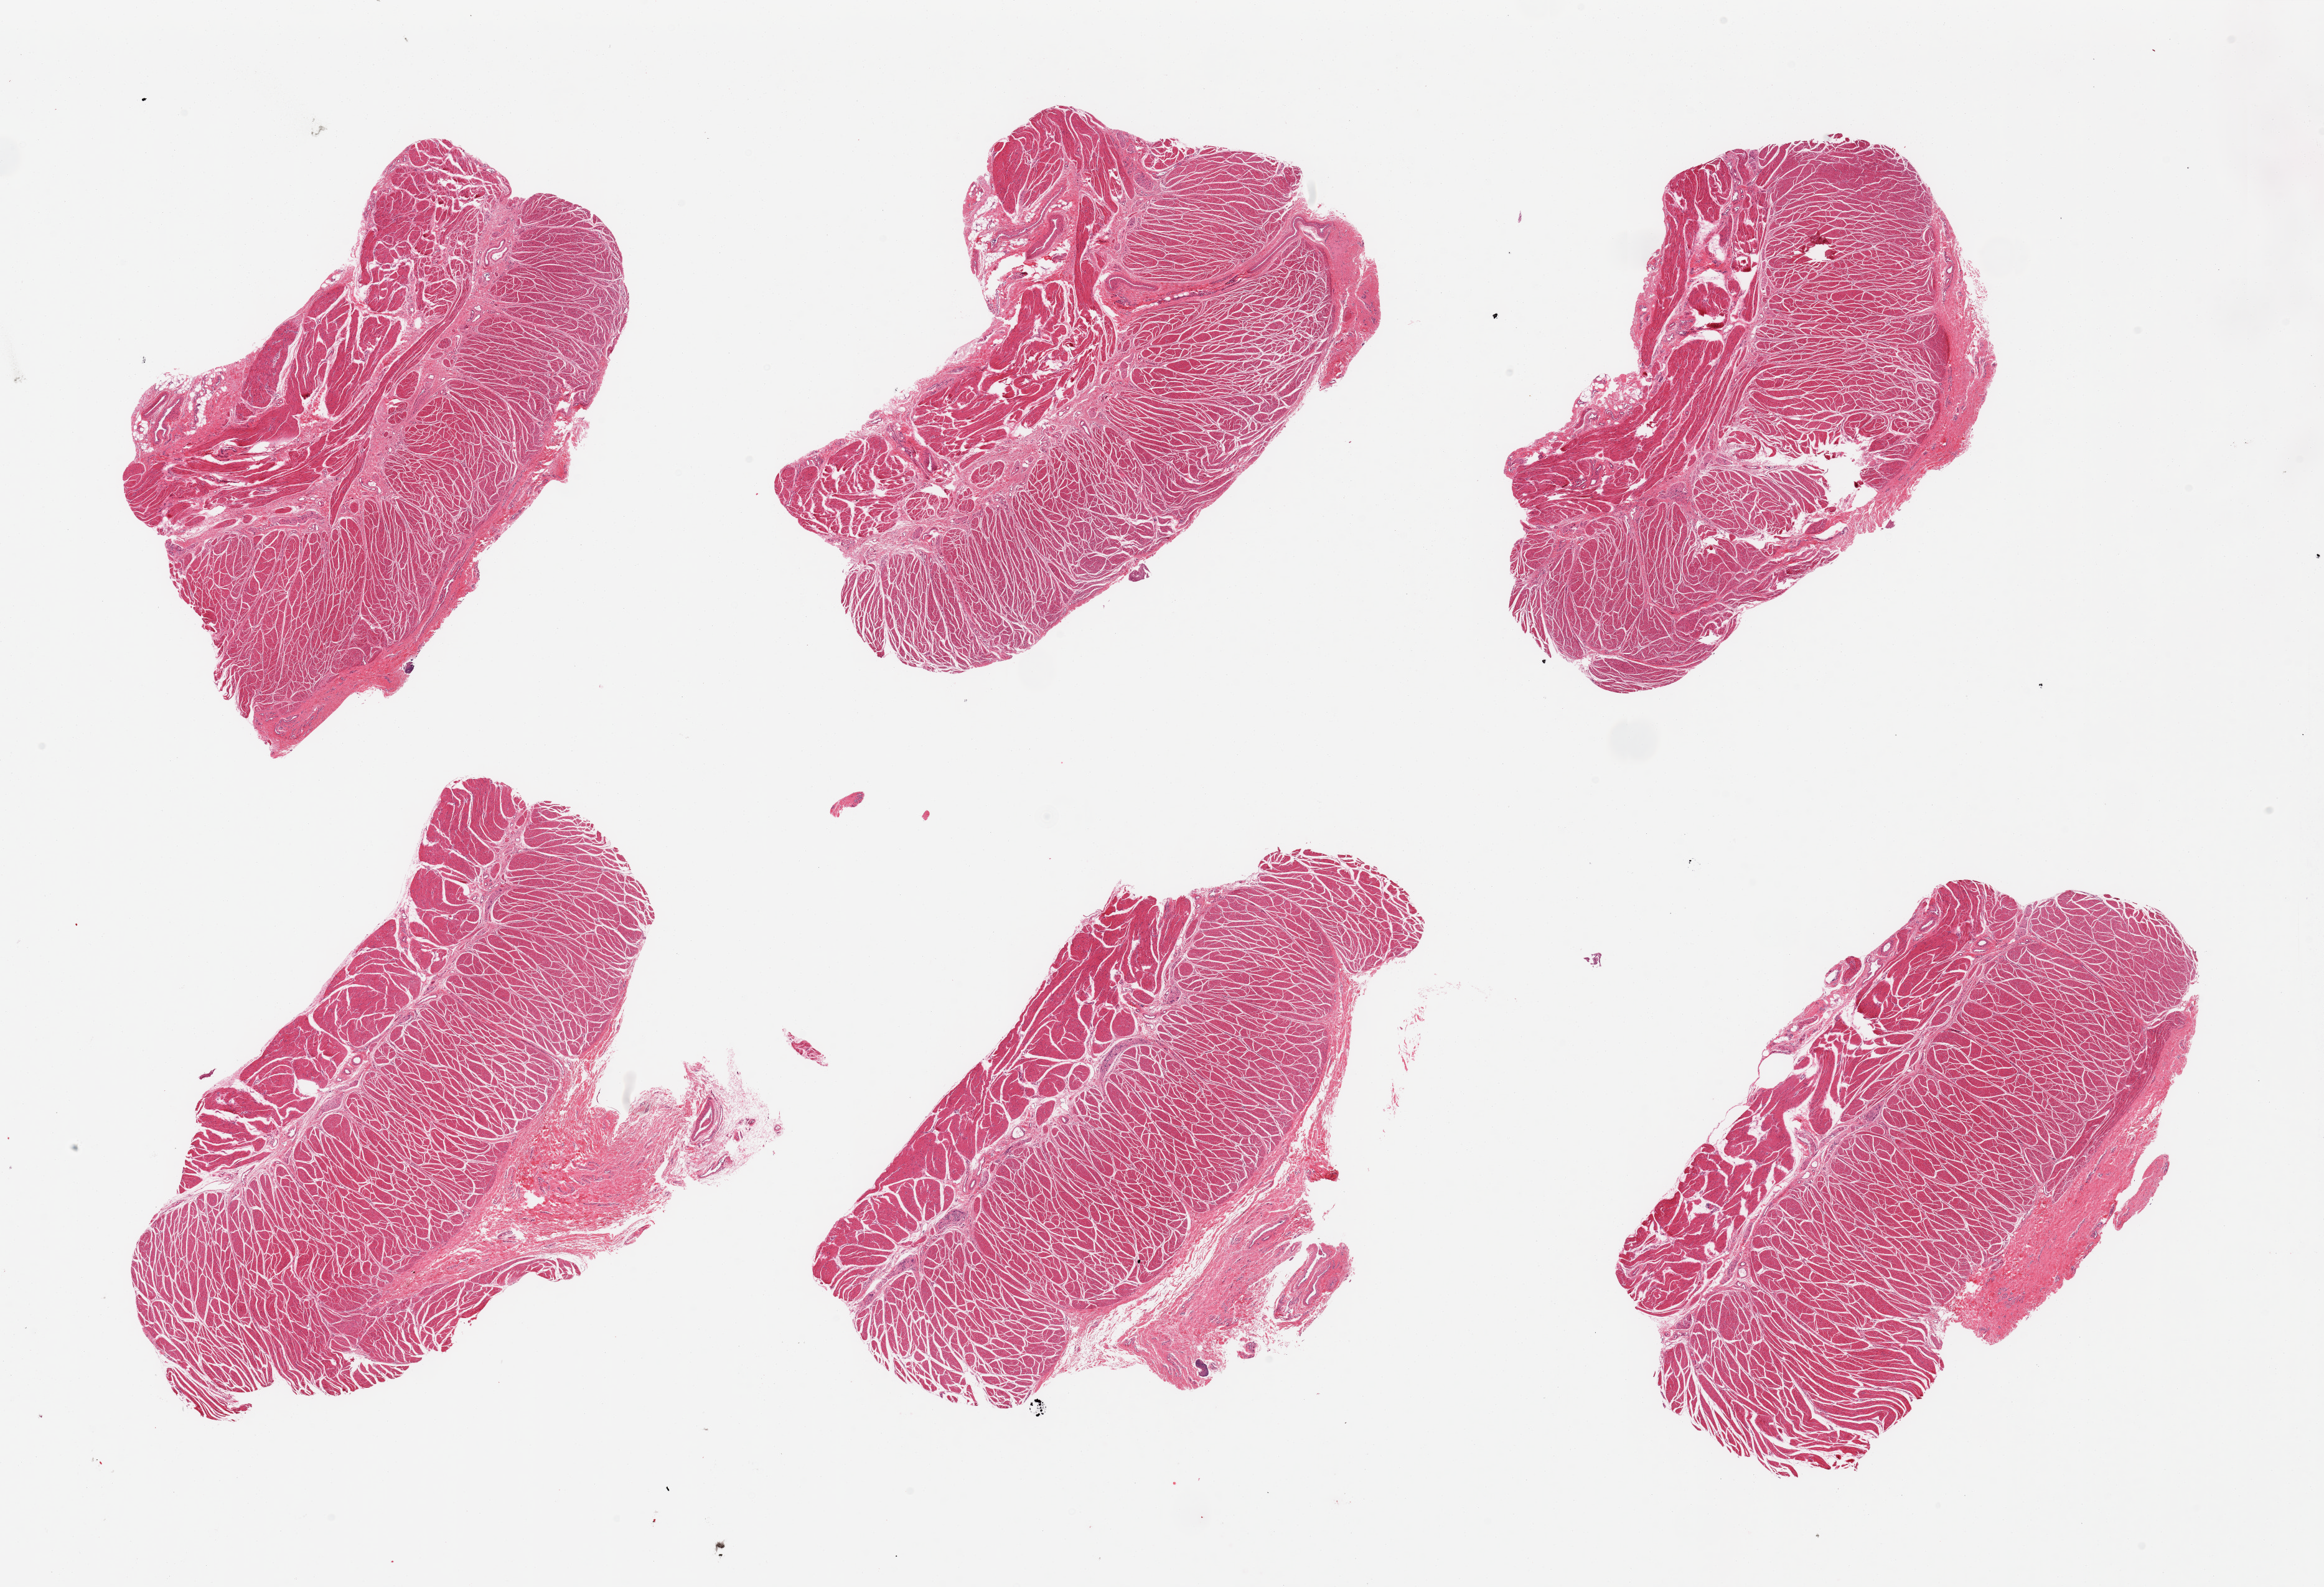
H&E whole-slide image, a low-resolution overview of the entire scanned area, about 29.5 x 20.2 mm (from a 20x scan), PAXgene-fixed paraffin-embedded (PFPE) section, section of gastroesophageal junction (target tissue), tissue donor sample.
Review note (as recorded): 6 pieces, target muscularis, good specimens.